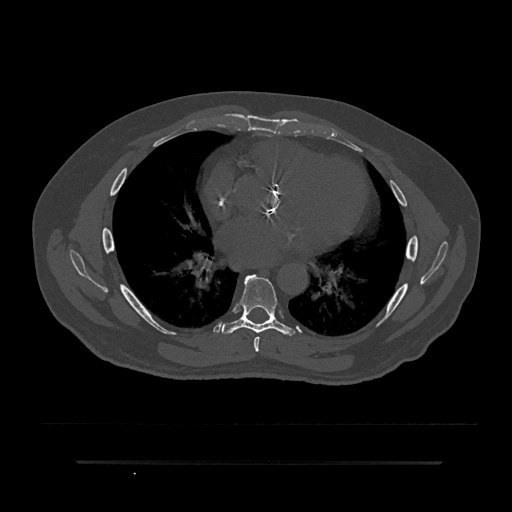
CT including the spine, one axial slice; slice 485 of 797 in the series (ordered by position); bone window (W 1800 / L 400 HU); 512 × 512 image matrix. Male patient, age 59 years. Case-level facts recorded for this patient, not image findings: primary cancer: bile ducts; vertebrae with lytic lesions (as recorded): T10.
Annotated regions visible in this slice (semi-automatic segmentation, software-assisted and operator-edited):
- T6 vertebra: bounding box [x1, y1, x2, y2] px = [254, 336, 260, 352]
- T7 vertebra: [222, 274, 295, 335]